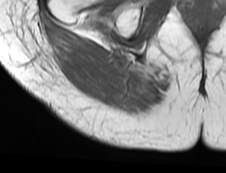
MRI of an extremity soft-tissue mass, one axial slice; MR volume resampled by the dataset authors to the PET/CT grid (not the native acquisition matrix); 226 × 173 image matrix, field of view 221 × 169 mm. Female patient. From the clinical record (not read from this slice): histological type: spindle cell suggestive of myxofibrosarcoma; grade: intermediate; site of the primary tumour: right buttock.
Outlined on this slice (expert contour drawn on MRI and transferred to this co-registered scan by the dataset authors):
- gross tumour volume (mass): bounding box (x1, y1, x2, y2) in pixels: (54, 44, 66, 61)